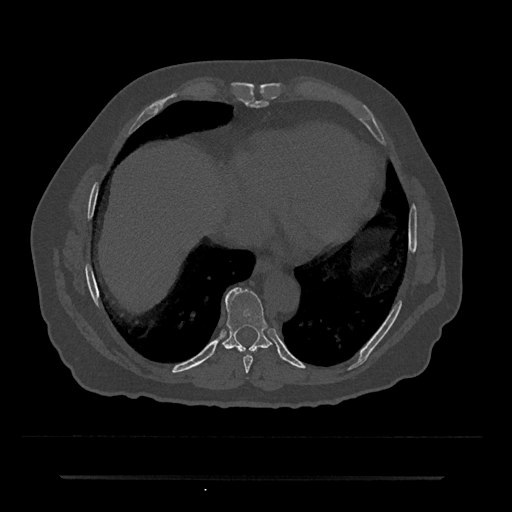
CT including the spine, one axial slice; position 293 of 797 along the scan axis; bone window (W 1800 / L 400 HU); 0.5 mm slice thickness; 512 × 512 image matrix. Patient: male, 69 years. From the clinical record (not read from this slice): primary cancer: prostate.
Outlined on this slice (semi-automatically segmented with operator editing):
- T8 vertebra: bounding box [x1, y1, x2, y2] px = [243, 355, 253, 373]
- T9 vertebra: [223, 287, 272, 352]